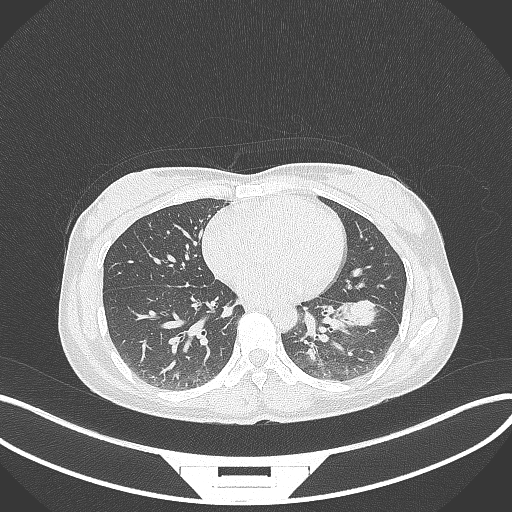
Chest CT, one axial slice. Position 32 of 244 along the scan axis. 120 kVp. Lung window (W 1500 / L -600 HU). 1 mm slice thickness. 512 × 512 image matrix, field of view 400 × 400 mm. Patient: female, 41 years. From the clinical record (not read from this slice): clinical TNM (as recorded): T2a N3 M1b.
Structures marked on this image (rectangle marked by the reading radiologist):
- lung tumour (recorded histology: adenocarcinoma): box from (x=337, y=294) to (x=387, y=328) px